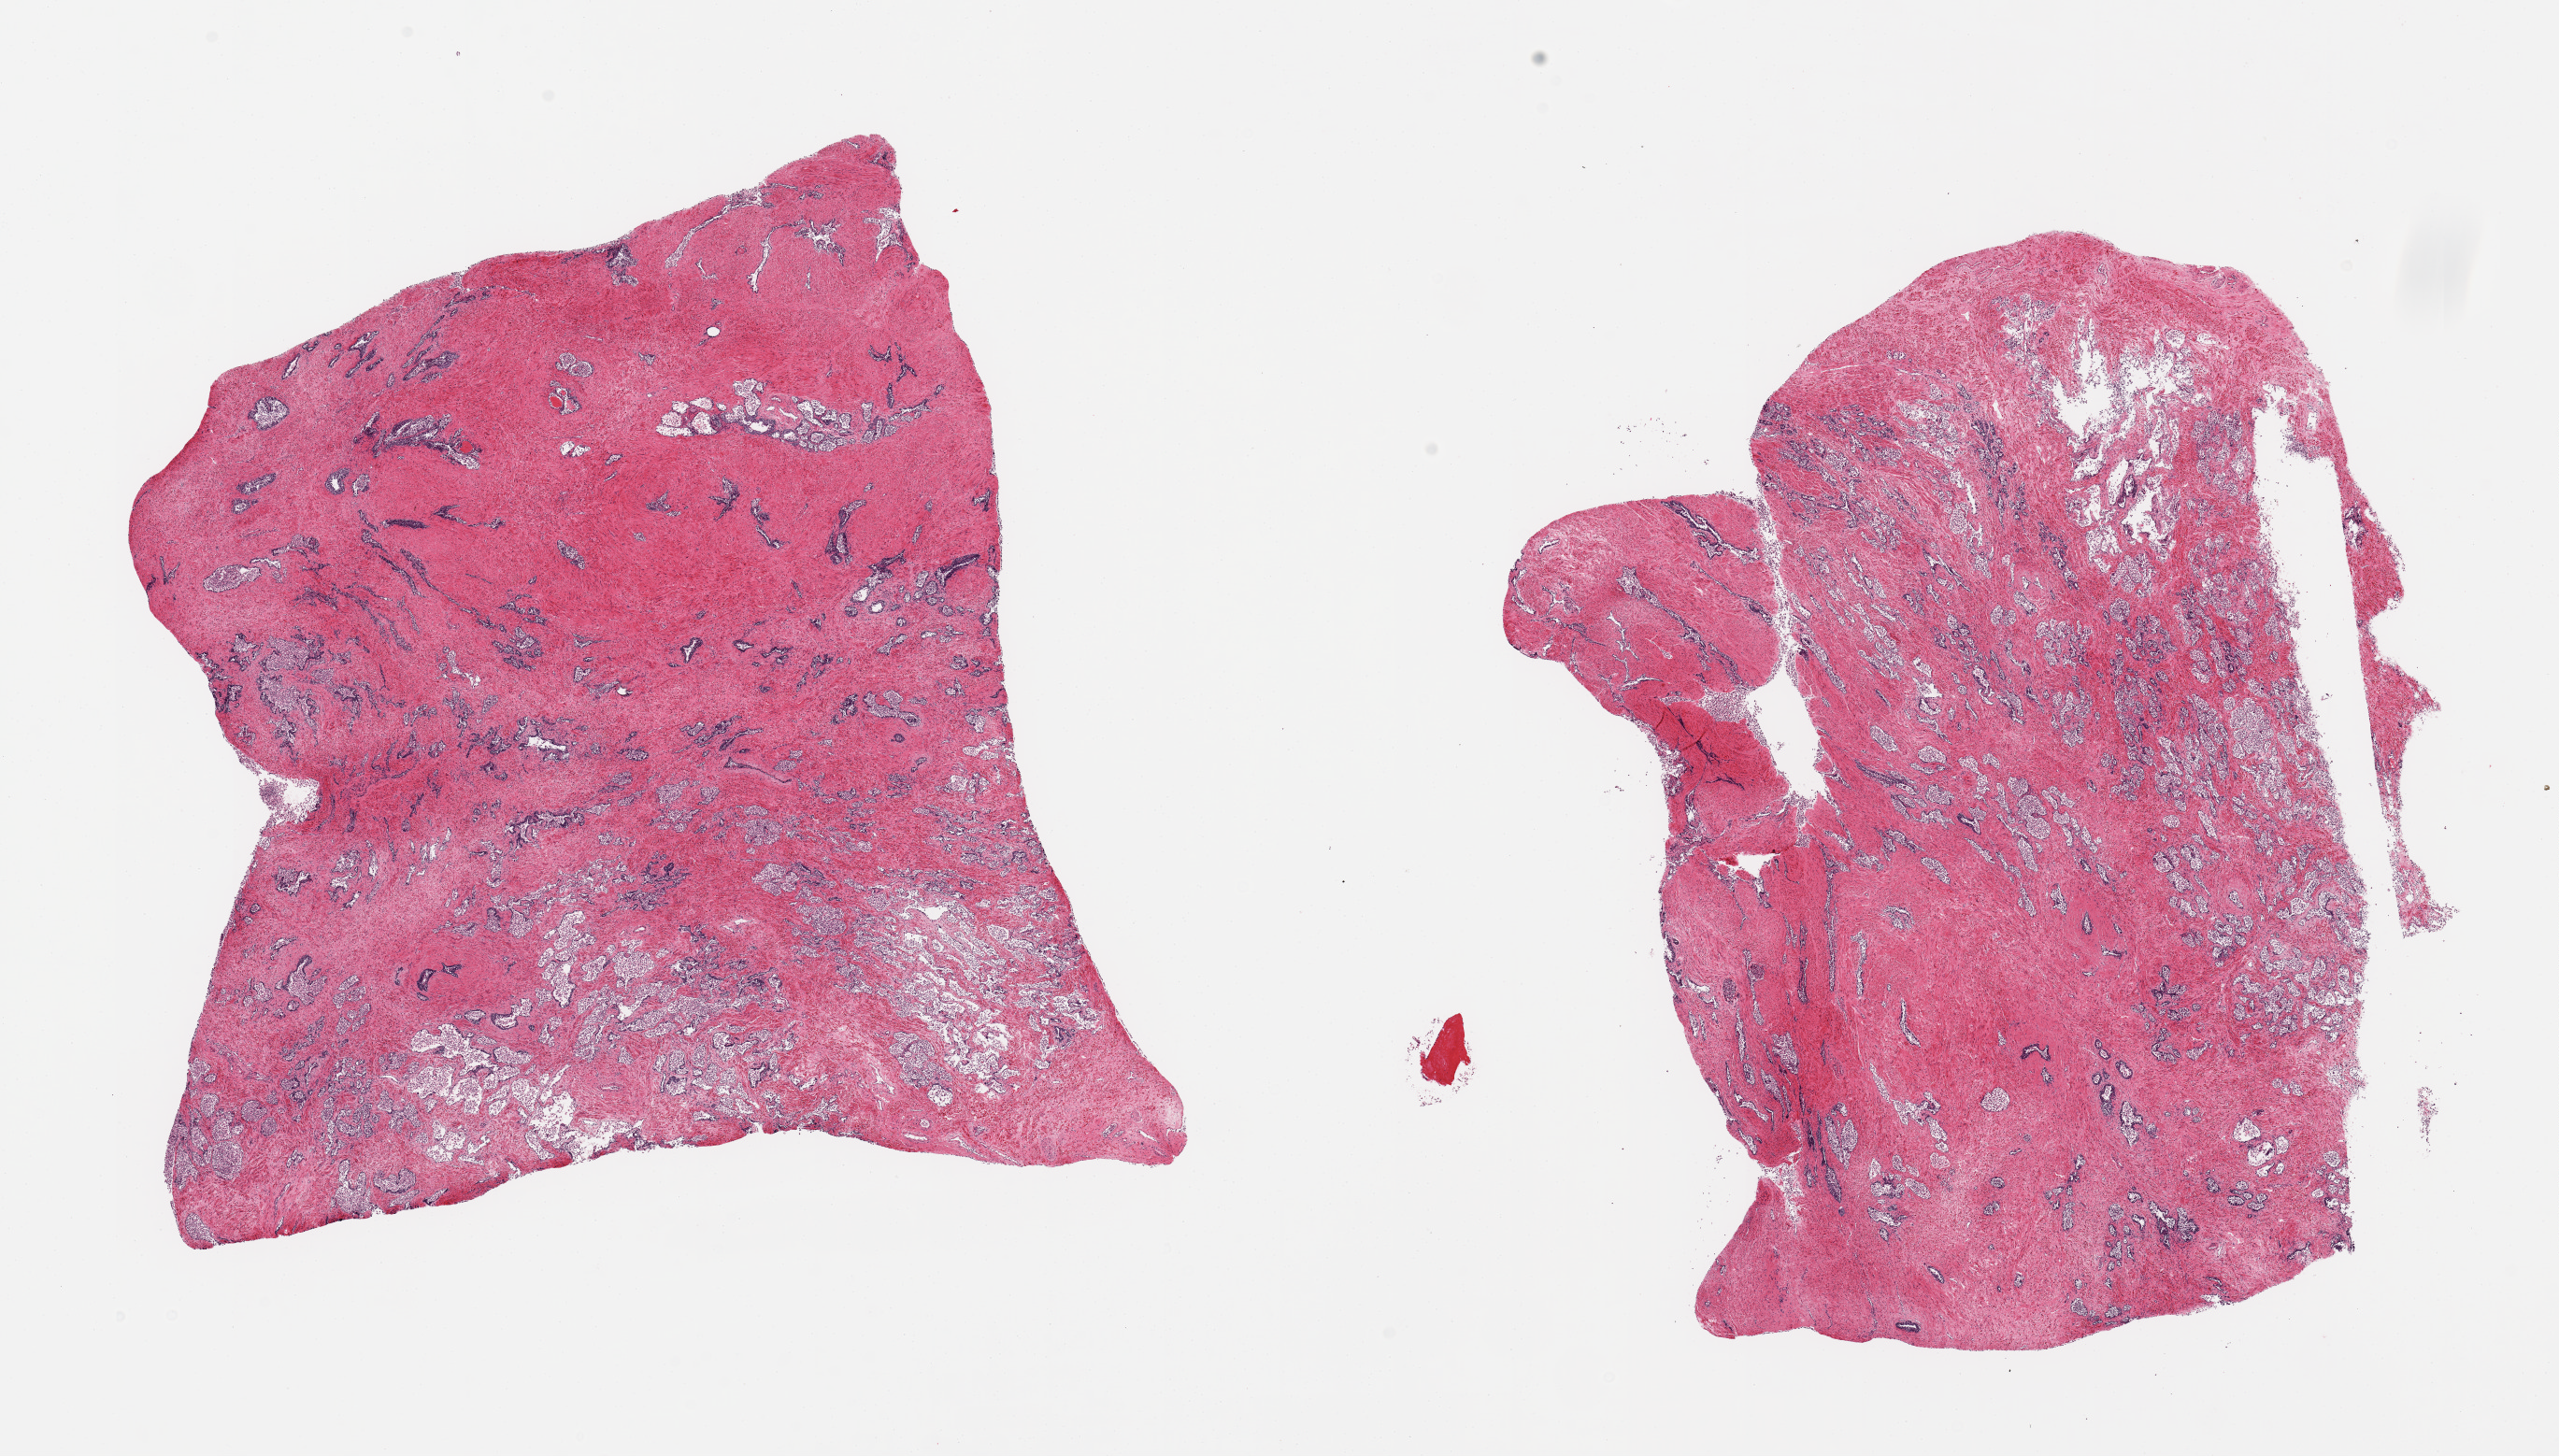
Haematoxylin and eosin whole-slide image, a low-resolution overview of the entire scanned area, about 21.7 x 12.3 mm (from a 20x scan); PAXgene-fixed paraffin-embedded (PFPE) section; section of prostate (target tissue); donor tissue sample. Male donor.
Pathologist's review note for this sample: 2 pieces, glandular elements totally autolyzed.